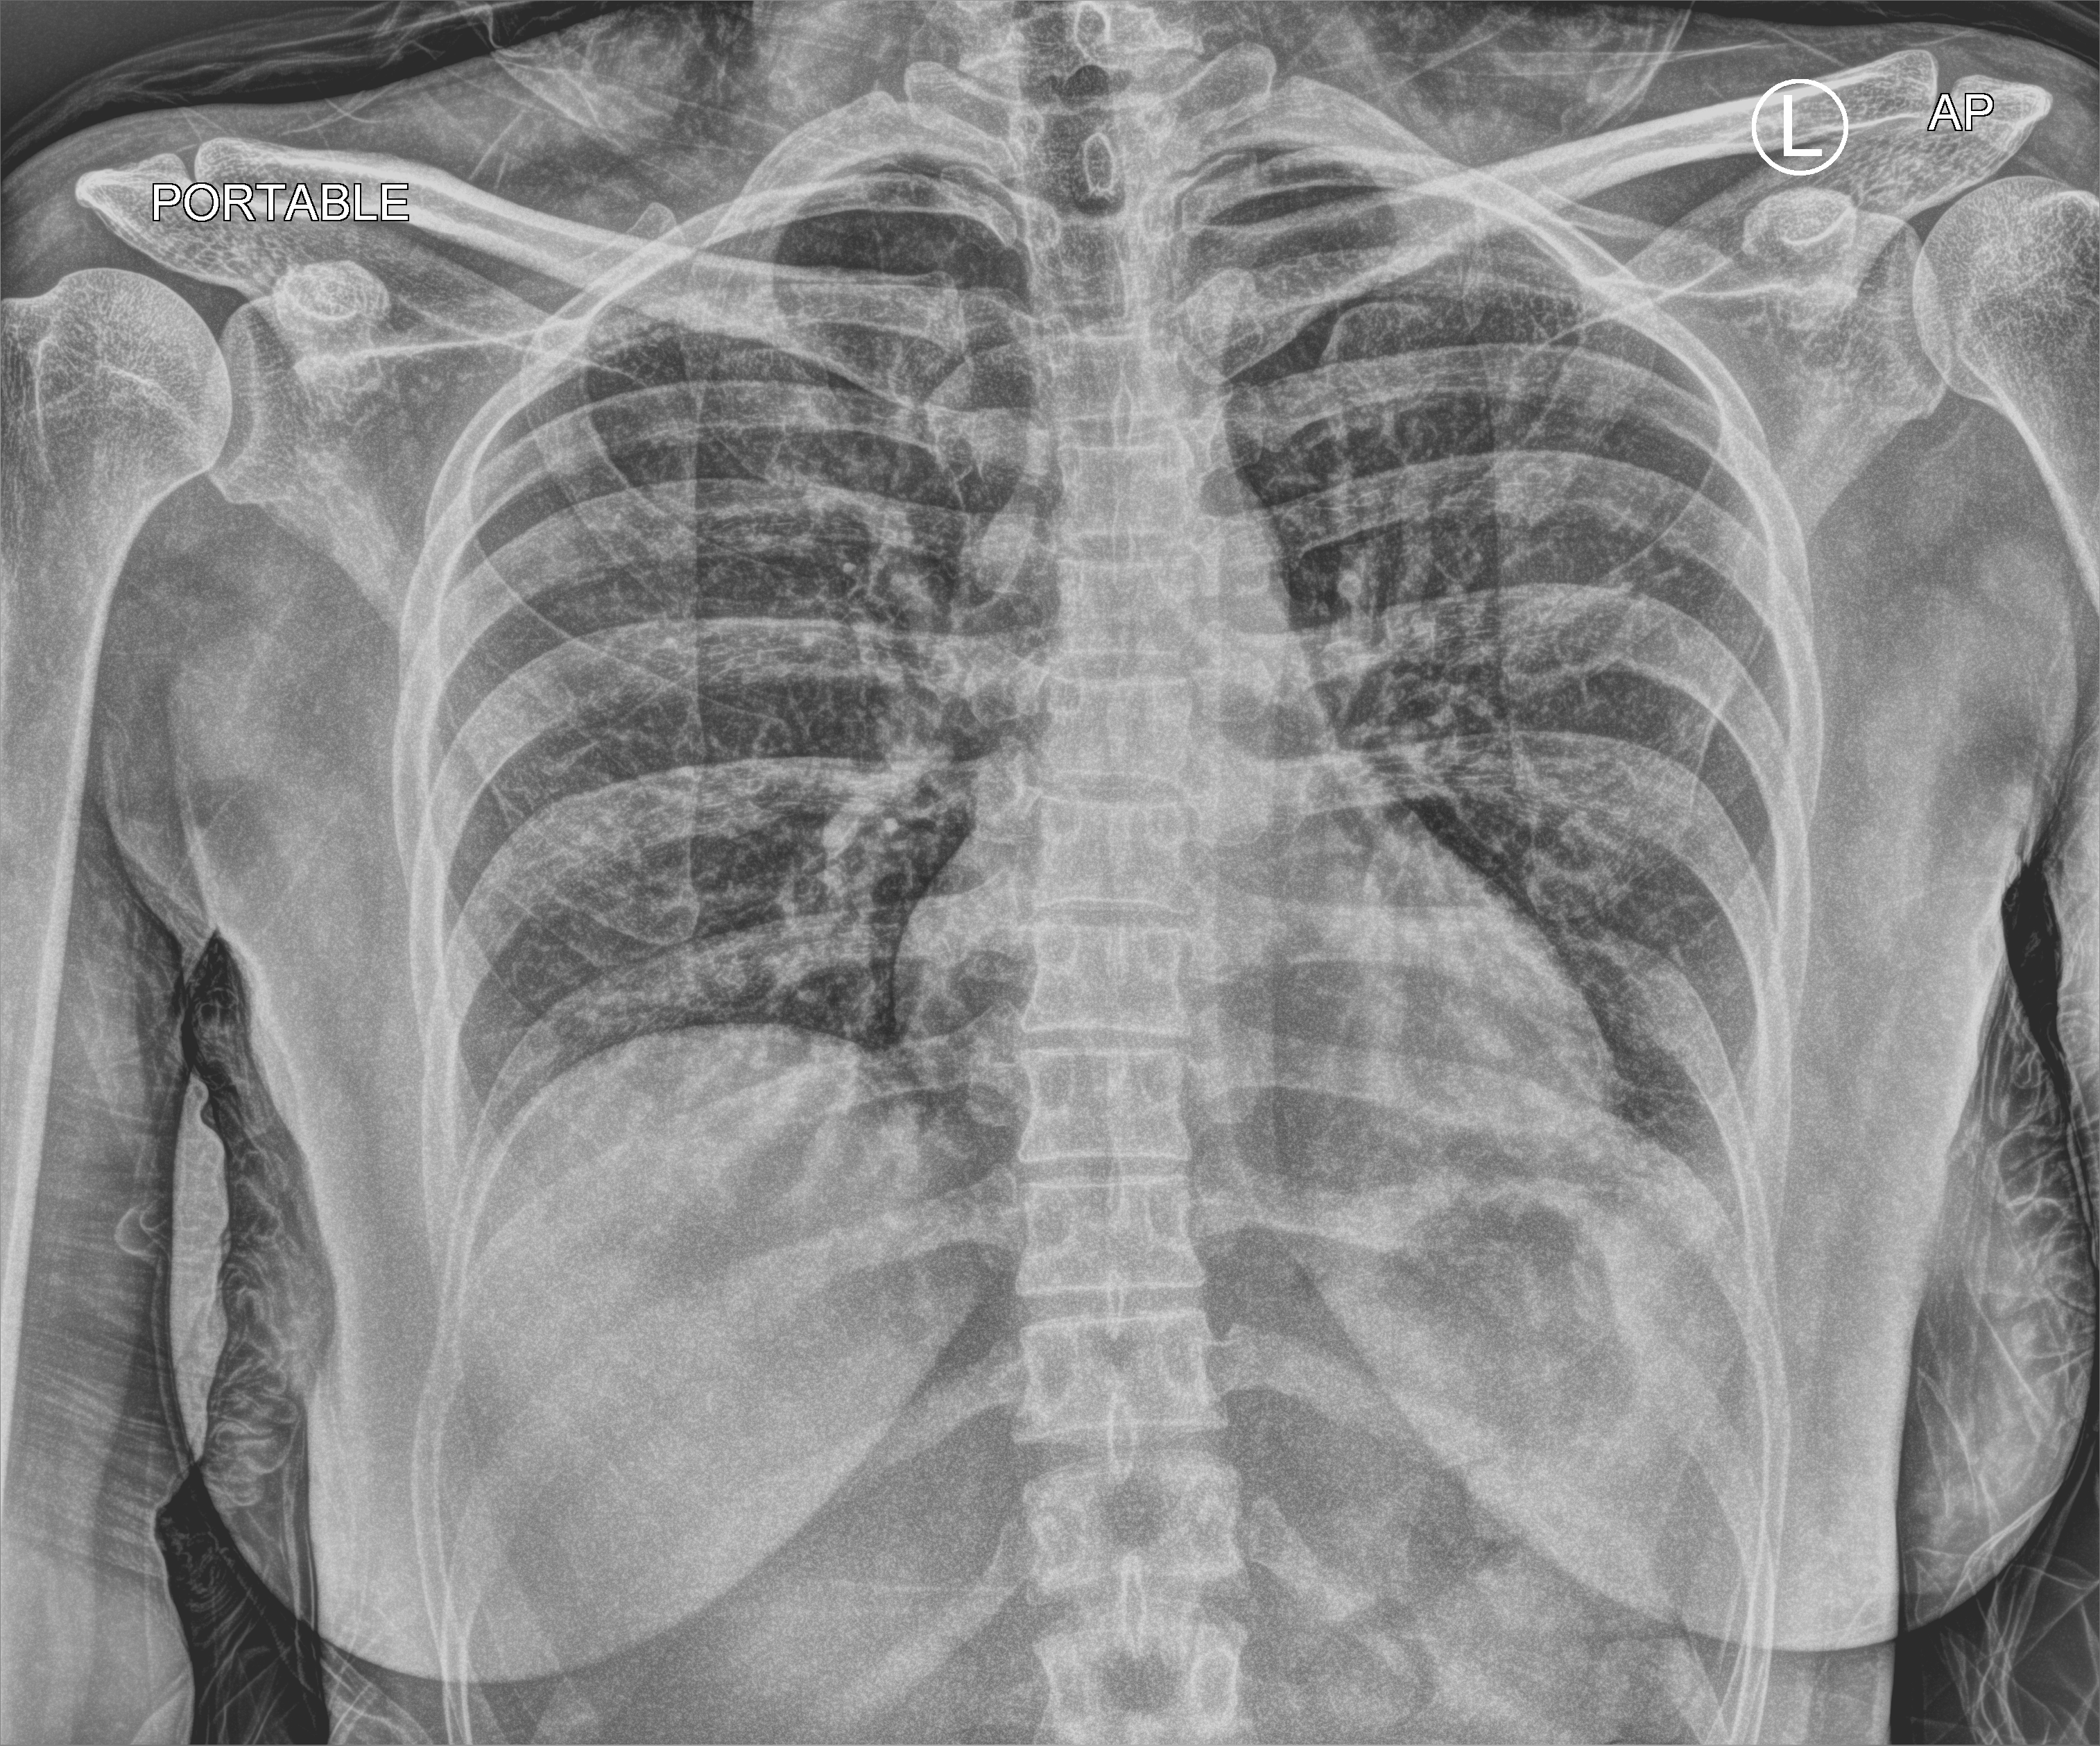
Portable chest radiograph. Patient hospitalised with COVID-19; female, aged 18–59 years.
From the hospital-stay record, not from the radiograph (when in the stay this image was taken is not recorded): admitted to intensive care during this hospital stay: no; mechanically ventilated during this hospital stay: no.